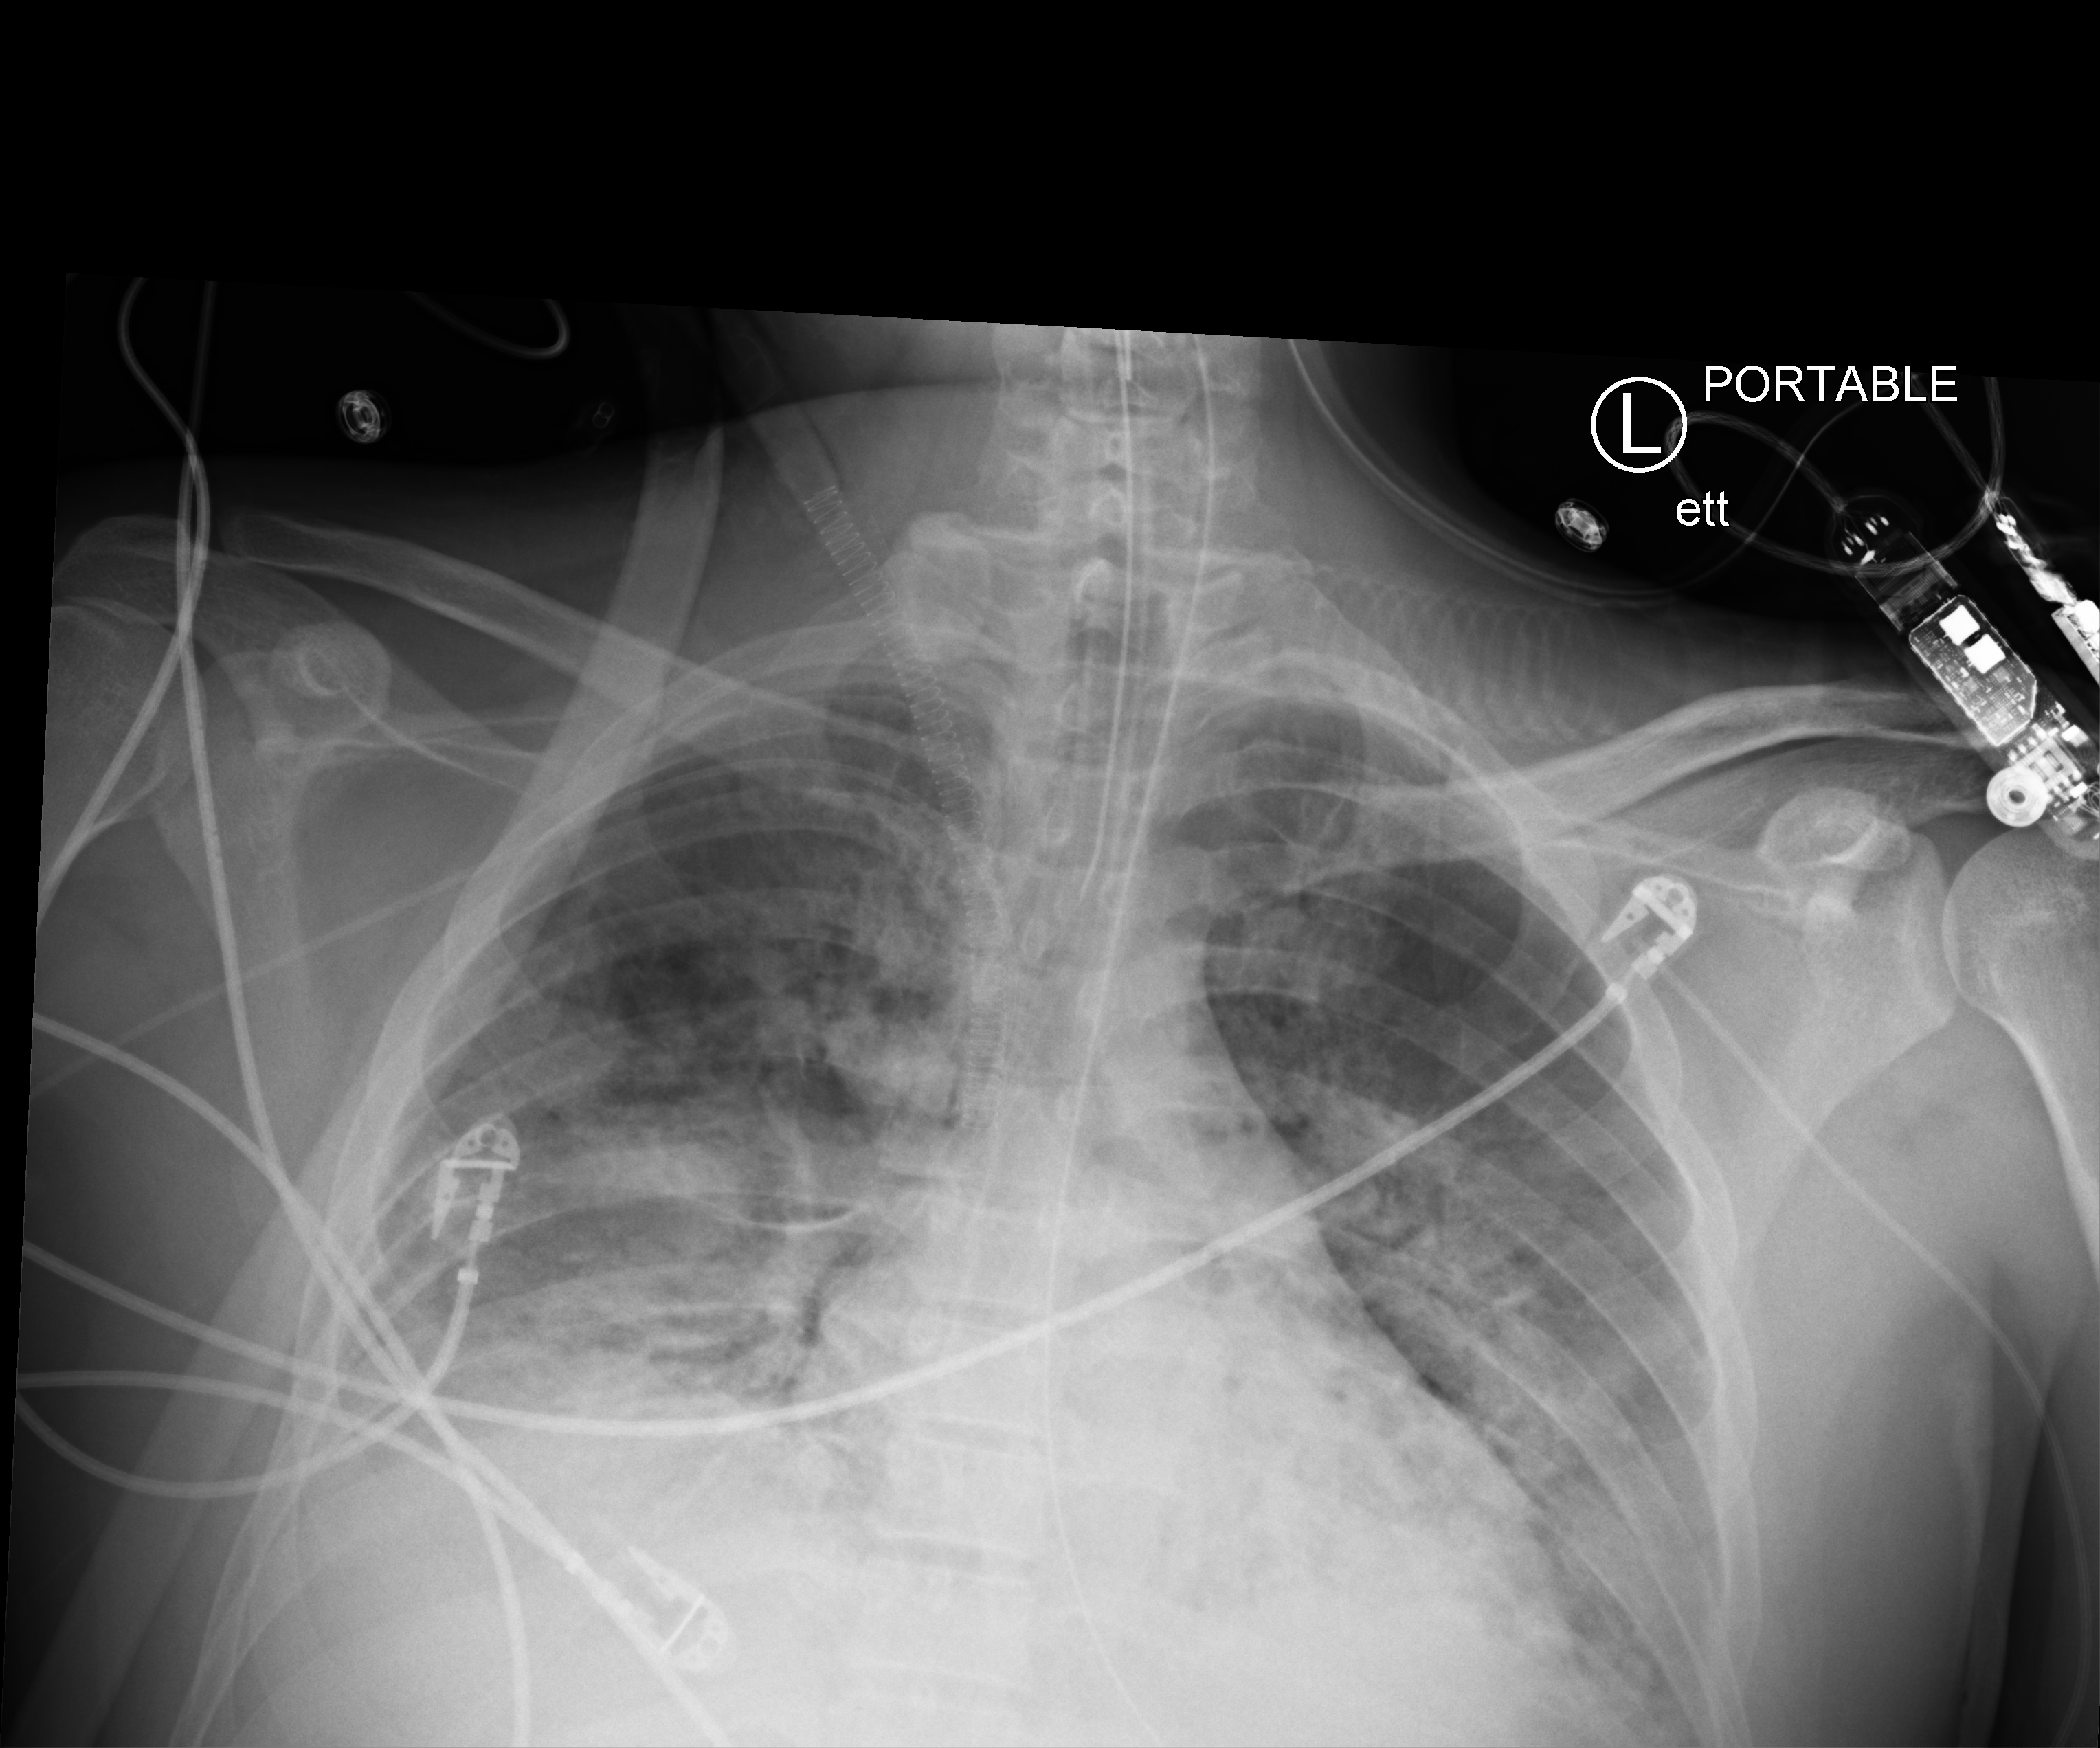
Bedside chest radiograph (computed radiography); anteroposterior (AP) projection. Adult patient hospitalised with COVID-19, age 18–59 years.
Admission-level facts for this patient (not findings on this image; timing relative to this image not recorded): mechanically ventilated during this hospital stay: yes.